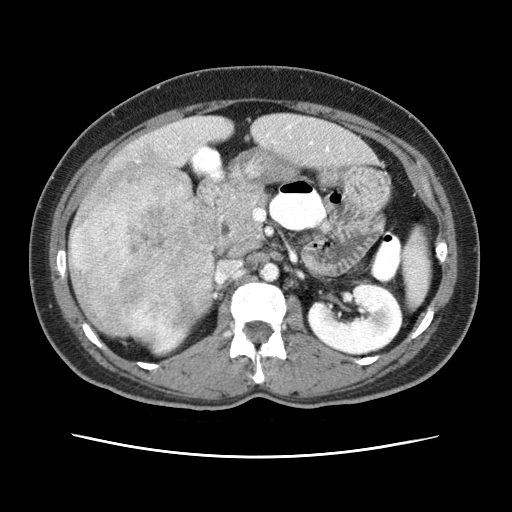
Contrast-enhanced abdominal CT (liver protocol), one axial slice. Position 19 of 79 along the scan axis. Reconstruction kernel STANDARD. 120 kVp. Soft-tissue window (W 400 / L 40 HU). 2.5 mm slice thickness. 512 × 512 image matrix, field of view 340 × 340 mm. From the clinical record (not read from this slice): diagnosis: hepatocellular carcinoma (patient treated with transarterial chemoembolisation; whether this scan precedes or follows treatment is not stated here); TNM stage (as recorded): Stage-I; Child-Pugh class: A.
Annotated regions visible in this slice (semi-automatically segmented with operator editing):
- abdominal aorta: bounding box <261,262,278,280> (left, top, right, bottom; pixels)
- liver parenchyma outside the tumour (the mass and vessels are separate outlines, so this box may not span the whole liver): <68,113,374,349>
- mass: <69,150,222,339>
- liver vessels: <169,125,329,151>